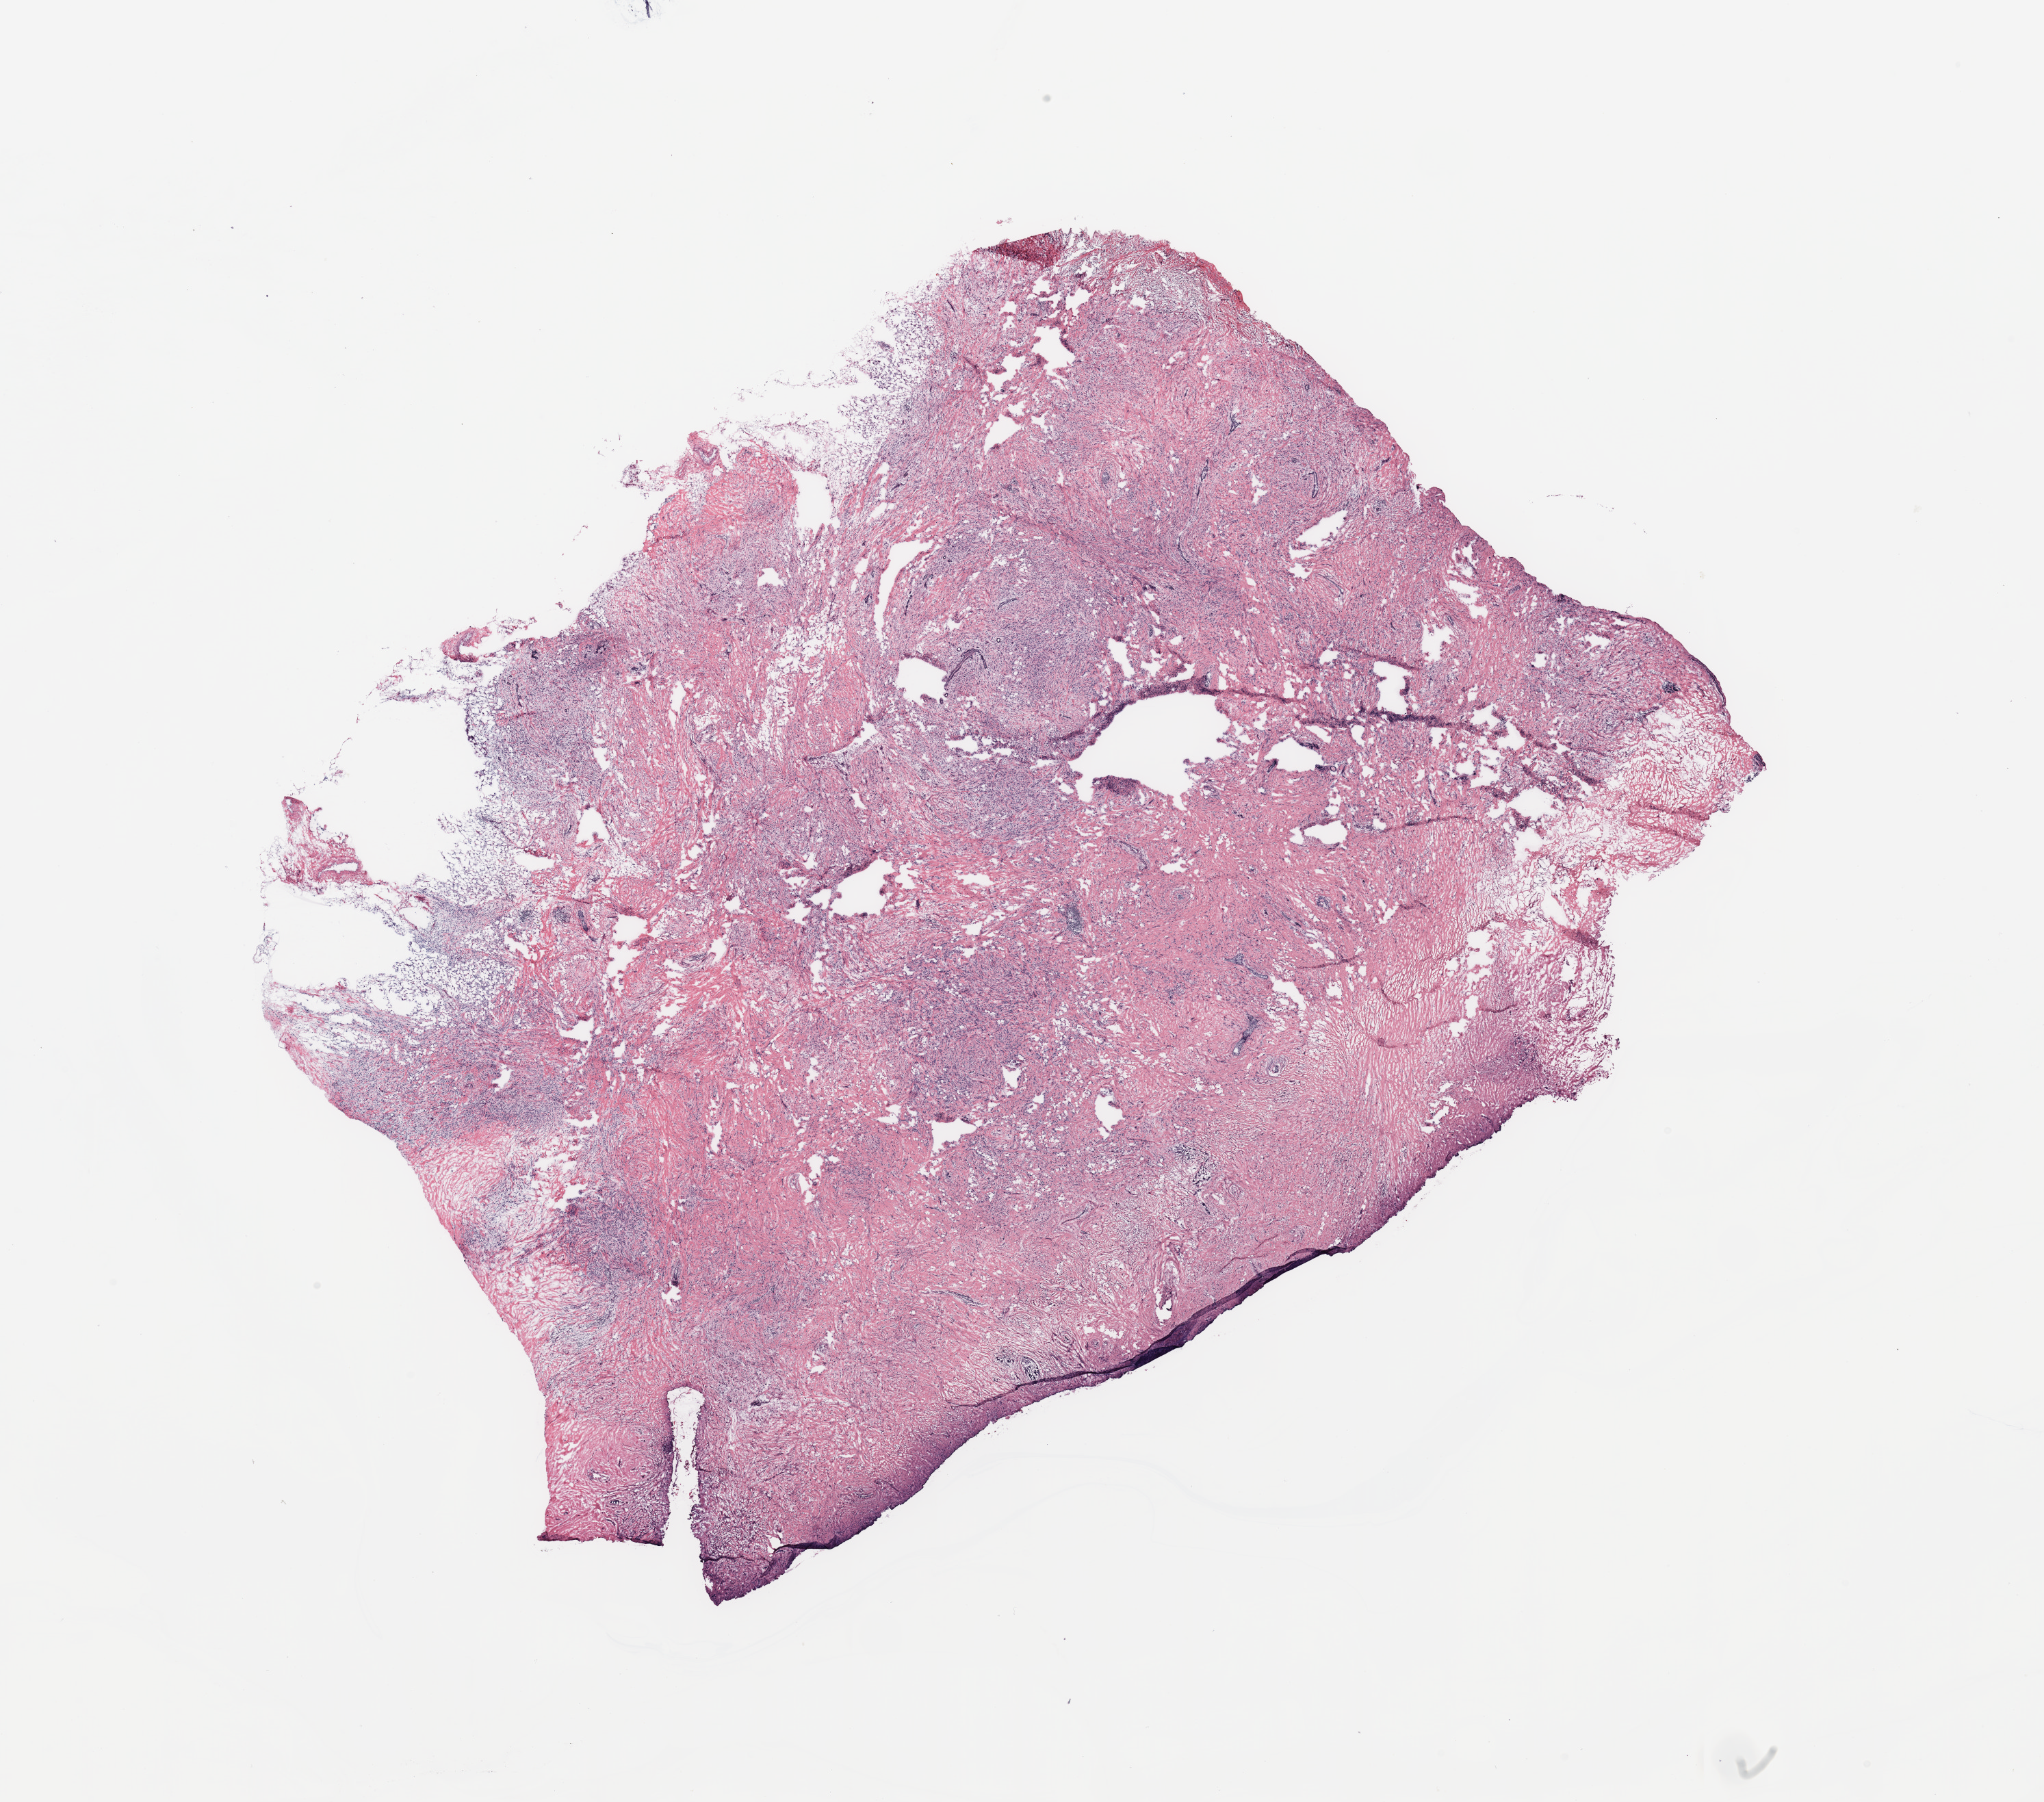
Digitized H&E tissue section (whole slide) — low-resolution overview of the scanned area, about 23.6 x 20.8 mm, breast, tissue type not recorded.
Patient diagnosis (cohort enrolment): breast cancer (breast).